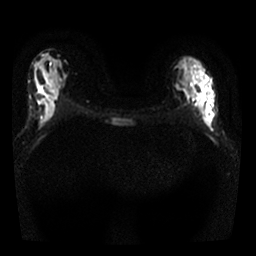
Breast MRI, one axial slice. Slice 11 of 25 in the series (ordered by position). Diffusion-weighted series; image 2 of 4 stored at this slice position (different b-values; order by instance number). 1.5 T. 4 mm slice thickness. 256 × 256 image matrix, field of view 300 × 300 mm. Female patient.
Structures marked on this image (expert manual segmentation):
- tumour on diffusion-weighted imaging: bounding box [x1, y1, x2, y2] px = [189, 83, 214, 128]